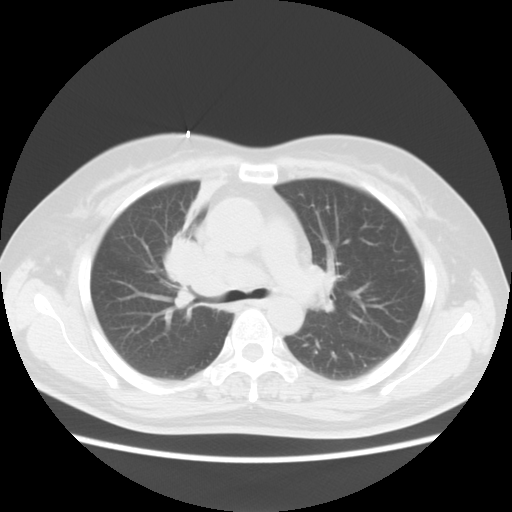
Chest CT, one axial slice. Position 7 of 18 along the scan axis. Reconstruction kernel STANDARD. 120 kVp. Lung window (W 1500 / L -600 HU). 512 × 512 image matrix, field of view 350 × 350 mm. Patient: female, 54 years. From the clinical record (not read from this slice): clinical TNM (as recorded): T2 N3 M0.
Structures marked on this image (rectangle marked by the reading radiologist):
- lung tumour (recorded histology: small cell carcinoma): bounding box (x1, y1, x2, y2) in pixels: (157, 239, 213, 312)